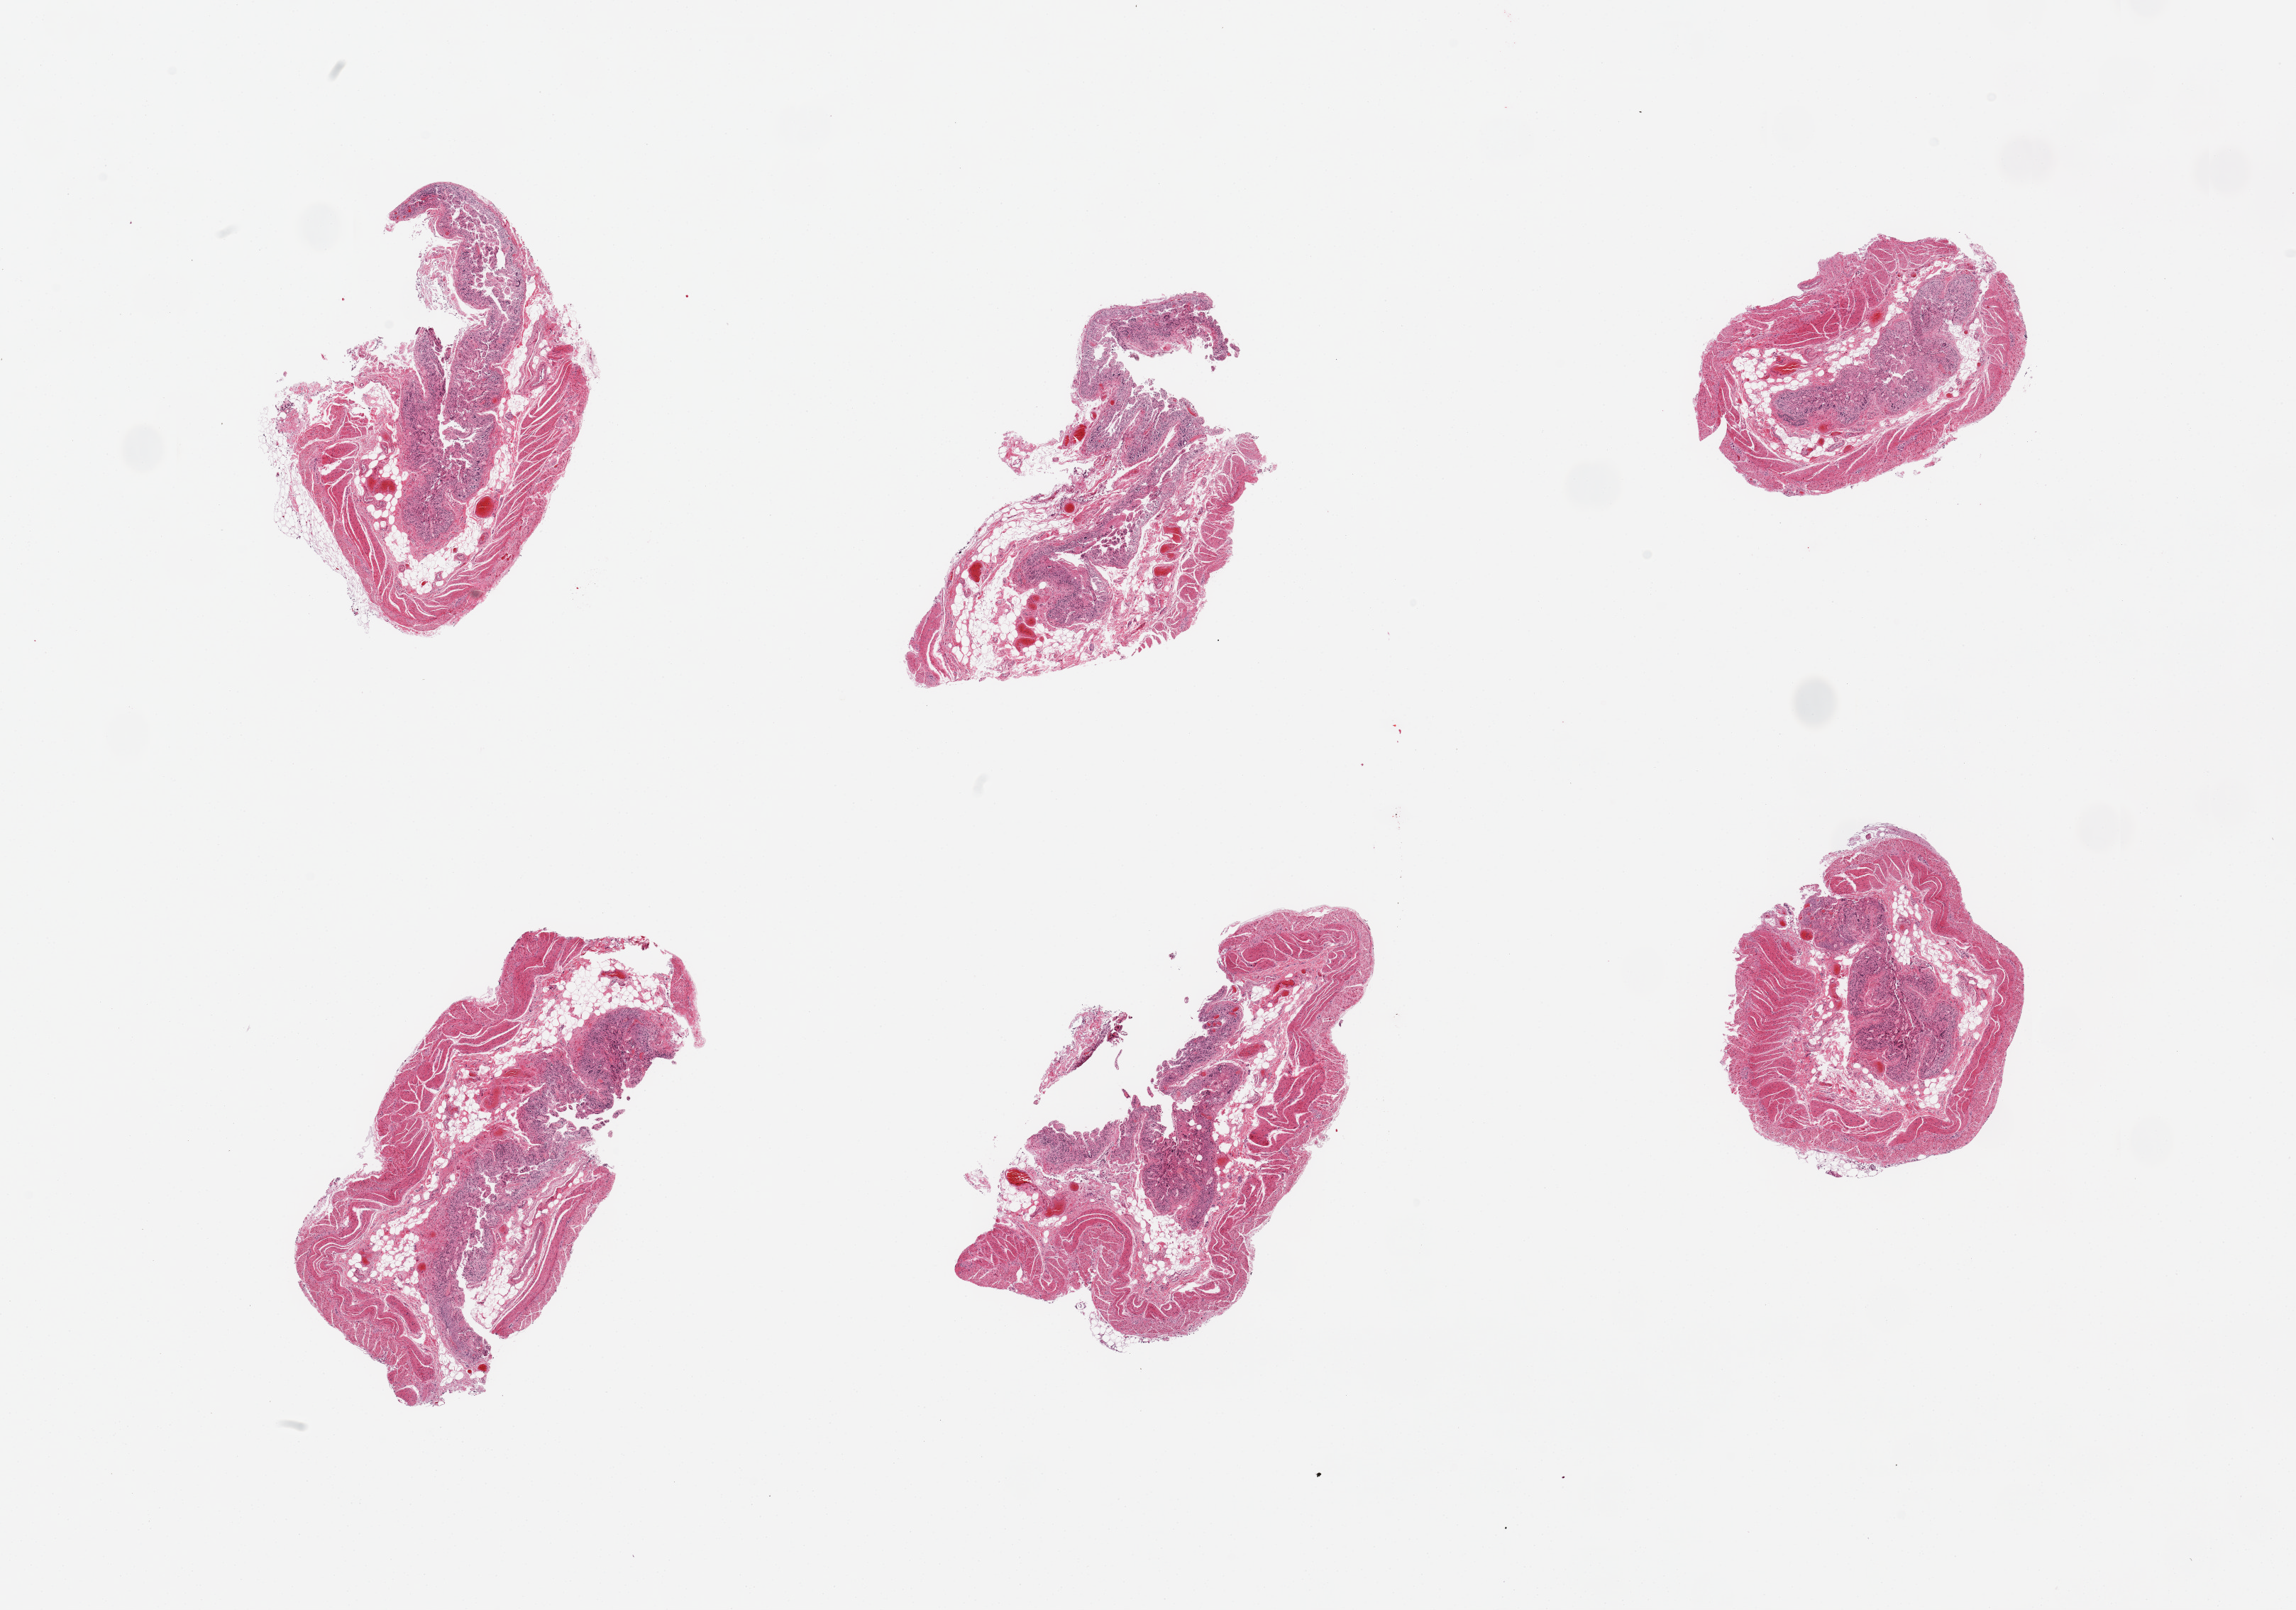
Digitized haematoxylin and eosin-stained section — shown as a low-resolution overview of the whole scanned area (about 25.6 x 17.9 mm), PAXgene-fixed, paraffin-embedded tissue, target tissue: transverse colon, donor tissue sample.
* review note (as recorded): 6 pieces; autolyzed small intestine, but no significant lymphoid tissue